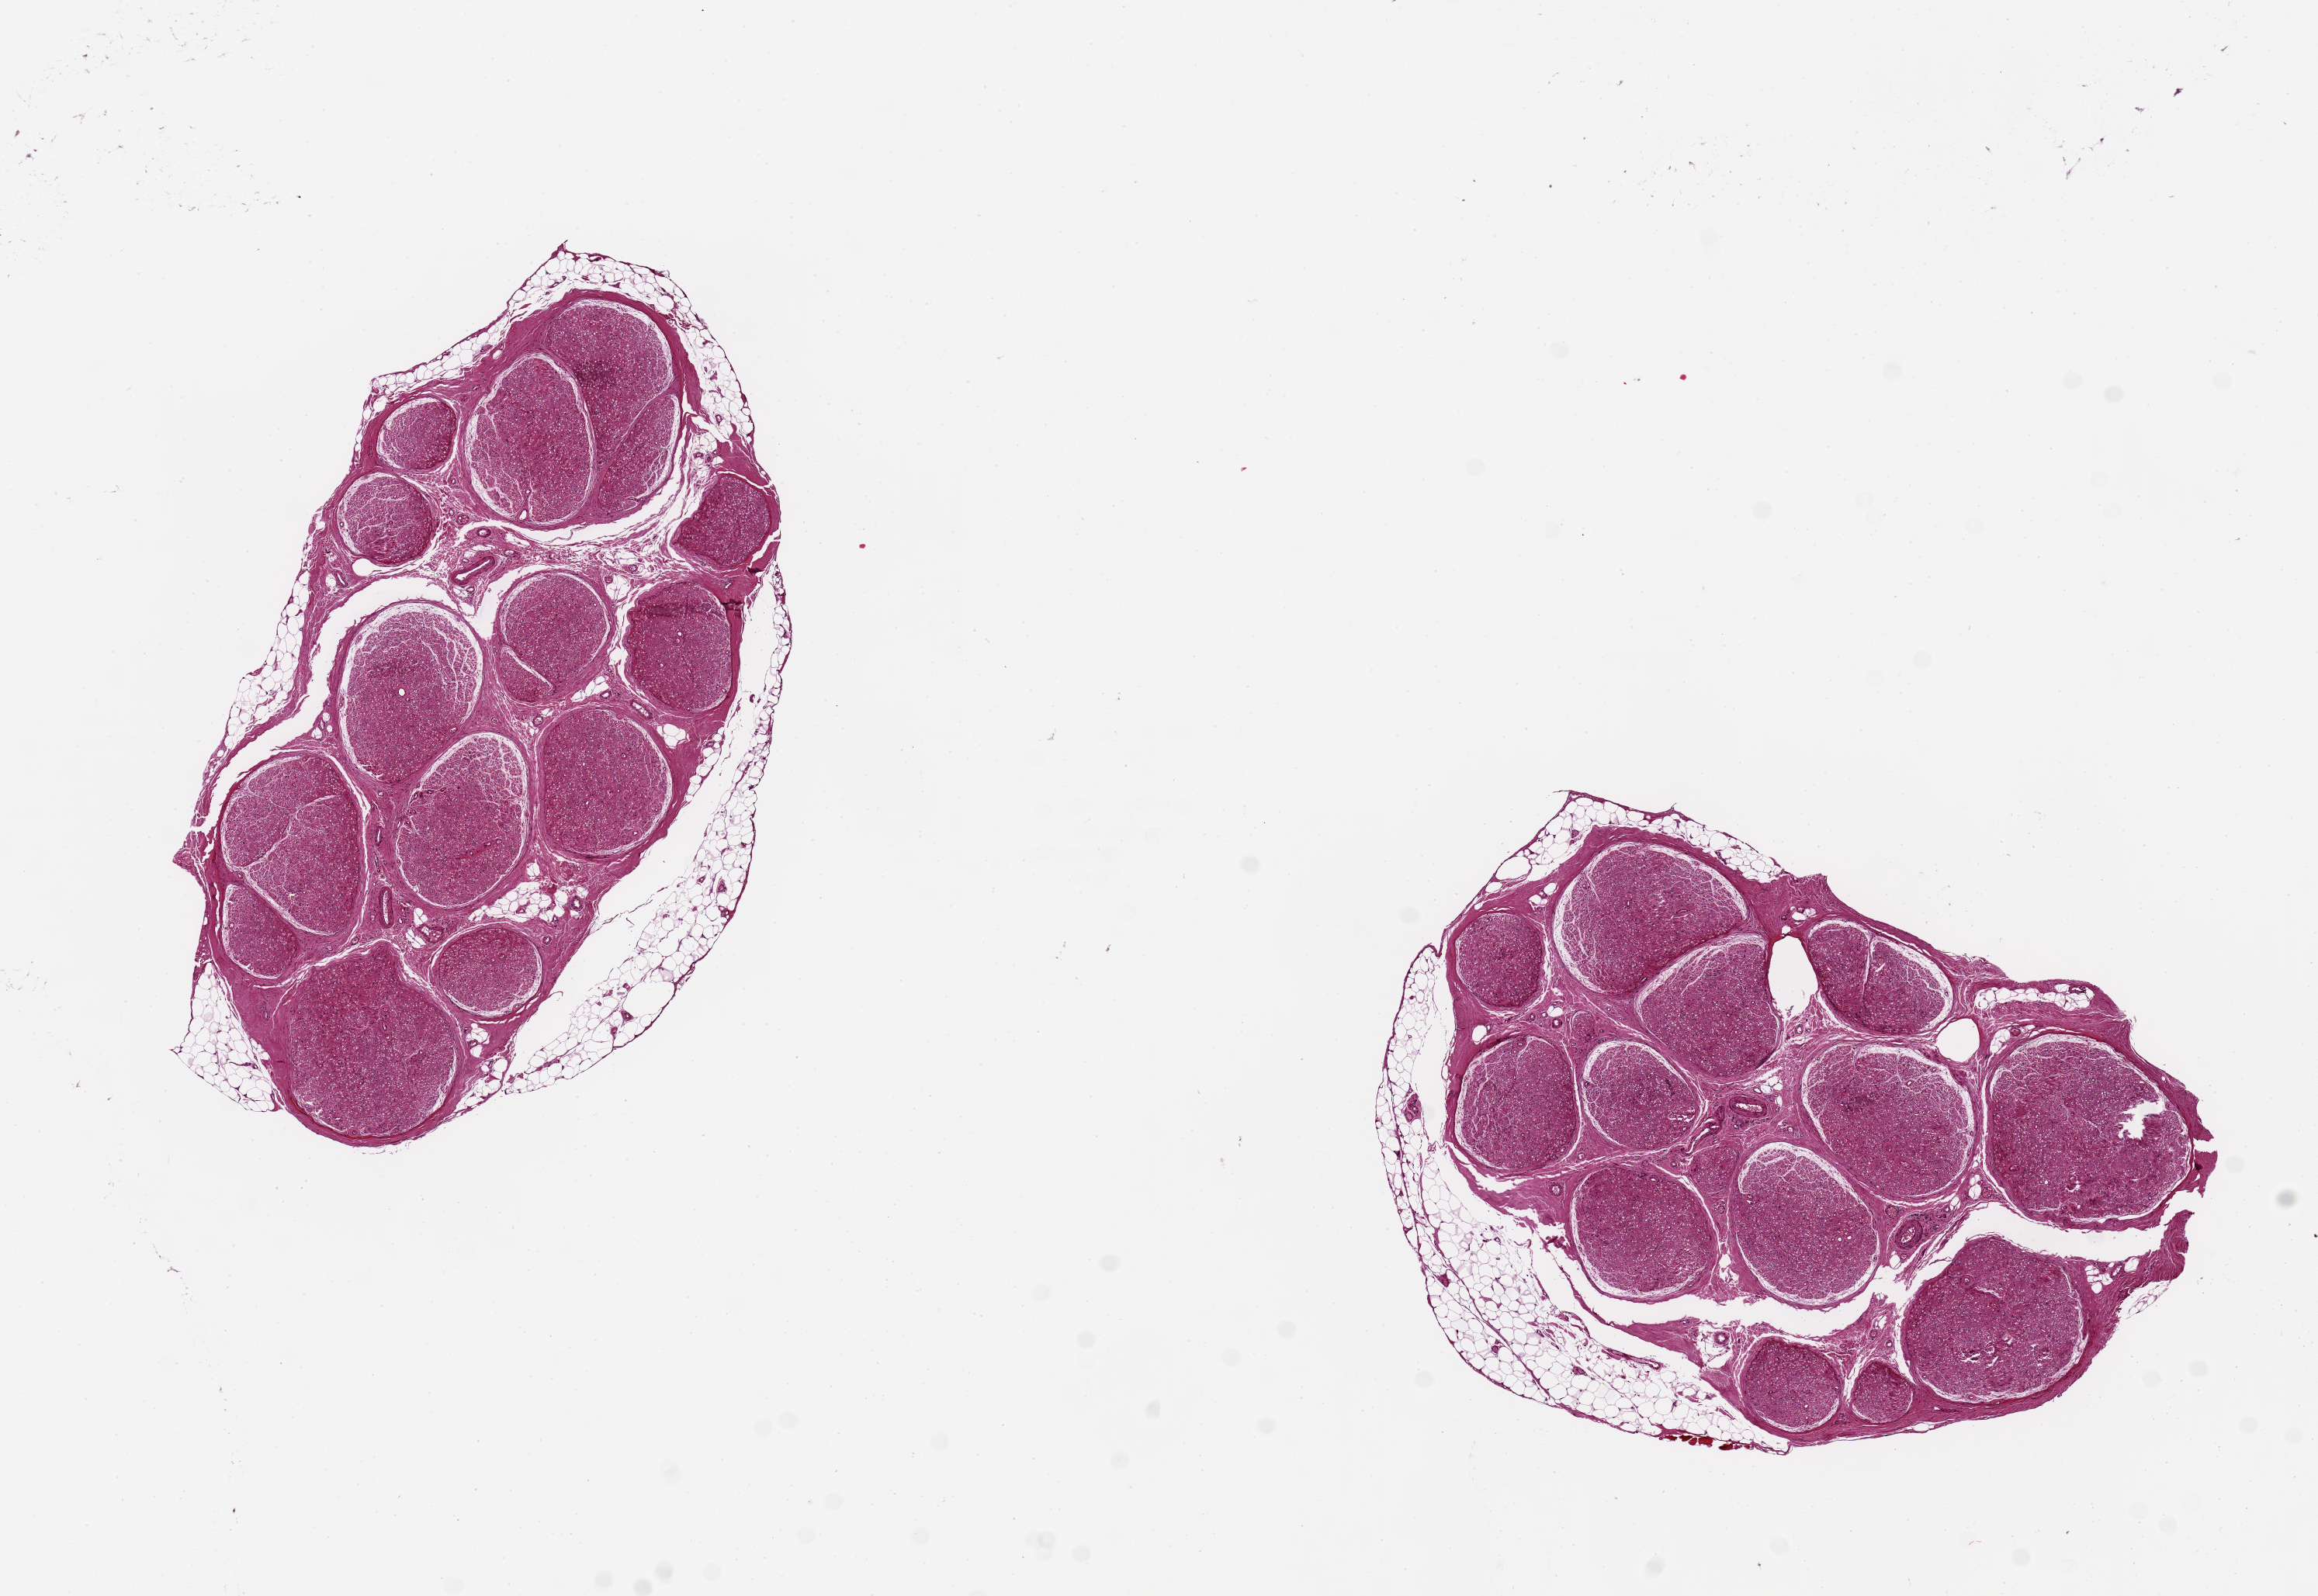
Whole-slide image, H&E stain — a low-resolution overview of the entire scanned area, about 11.8 x 8.1 mm (from a 20x scan); PAXgene-fixed paraffin-embedded (PFPE) section; section of tibial nerve (target tissue); tissue donor sample.
Pathologist's review note for this sample: 2 aliquots, ~4.5x3mm. Discontinuous rim of fat, up to ~0.5mm.